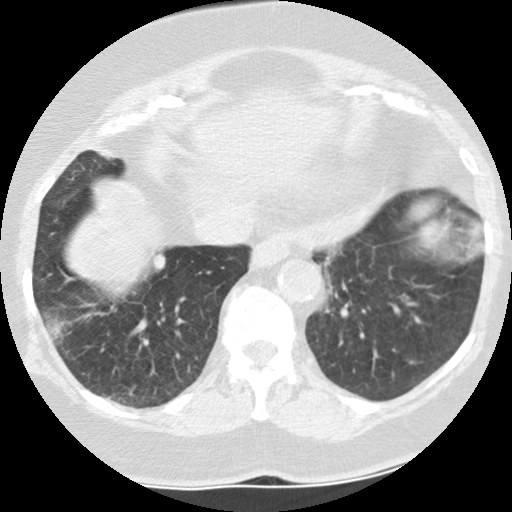
Low-dose screening chest CT, one axial slice. Position 38 of 157 along the scan axis. Reconstruction kernel STANDARD. 120 kVp. Lung window (W 1500 / L -600 HU). 2.5 mm slice thickness. 512 × 512 image matrix.
Annotated regions visible in this slice (outlined manually by an expert reader):
- lesion 1 (tumor, lower lobe of right lung): bounding box <152,253,165,269> (left, top, right, bottom; pixels)